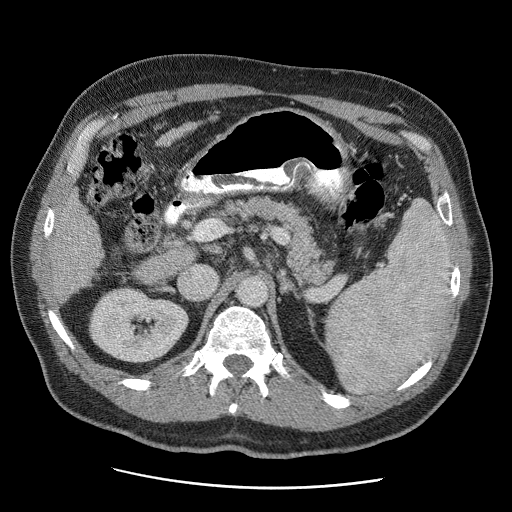
Contrast-enhanced abdominal CT (liver protocol), one axial slice; slice 18 of 81 in the series (ordered by position); soft-tissue window (W 400 / L 40 HU); 512 × 512 image matrix, field of view 380 × 380 mm. Case-level facts recorded for this patient, not image findings: diagnosis: hepatocellular carcinoma (patient treated with transarterial chemoembolisation; whether this scan precedes or follows treatment is not stated here); TNM stage (as recorded): Stage-IIIA; Child-Pugh class: A; tumour nodularity: multinodular; tumour size: 5.5 cm.
Annotated regions visible in this slice (semi-automatic segmentation, software-assisted and operator-edited):
- liver parenchyma outside the tumour (the mass and vessels are separate outlines, so this box may not span the whole liver): bounding box [x1, y1, x2, y2] px = [48, 188, 103, 301]